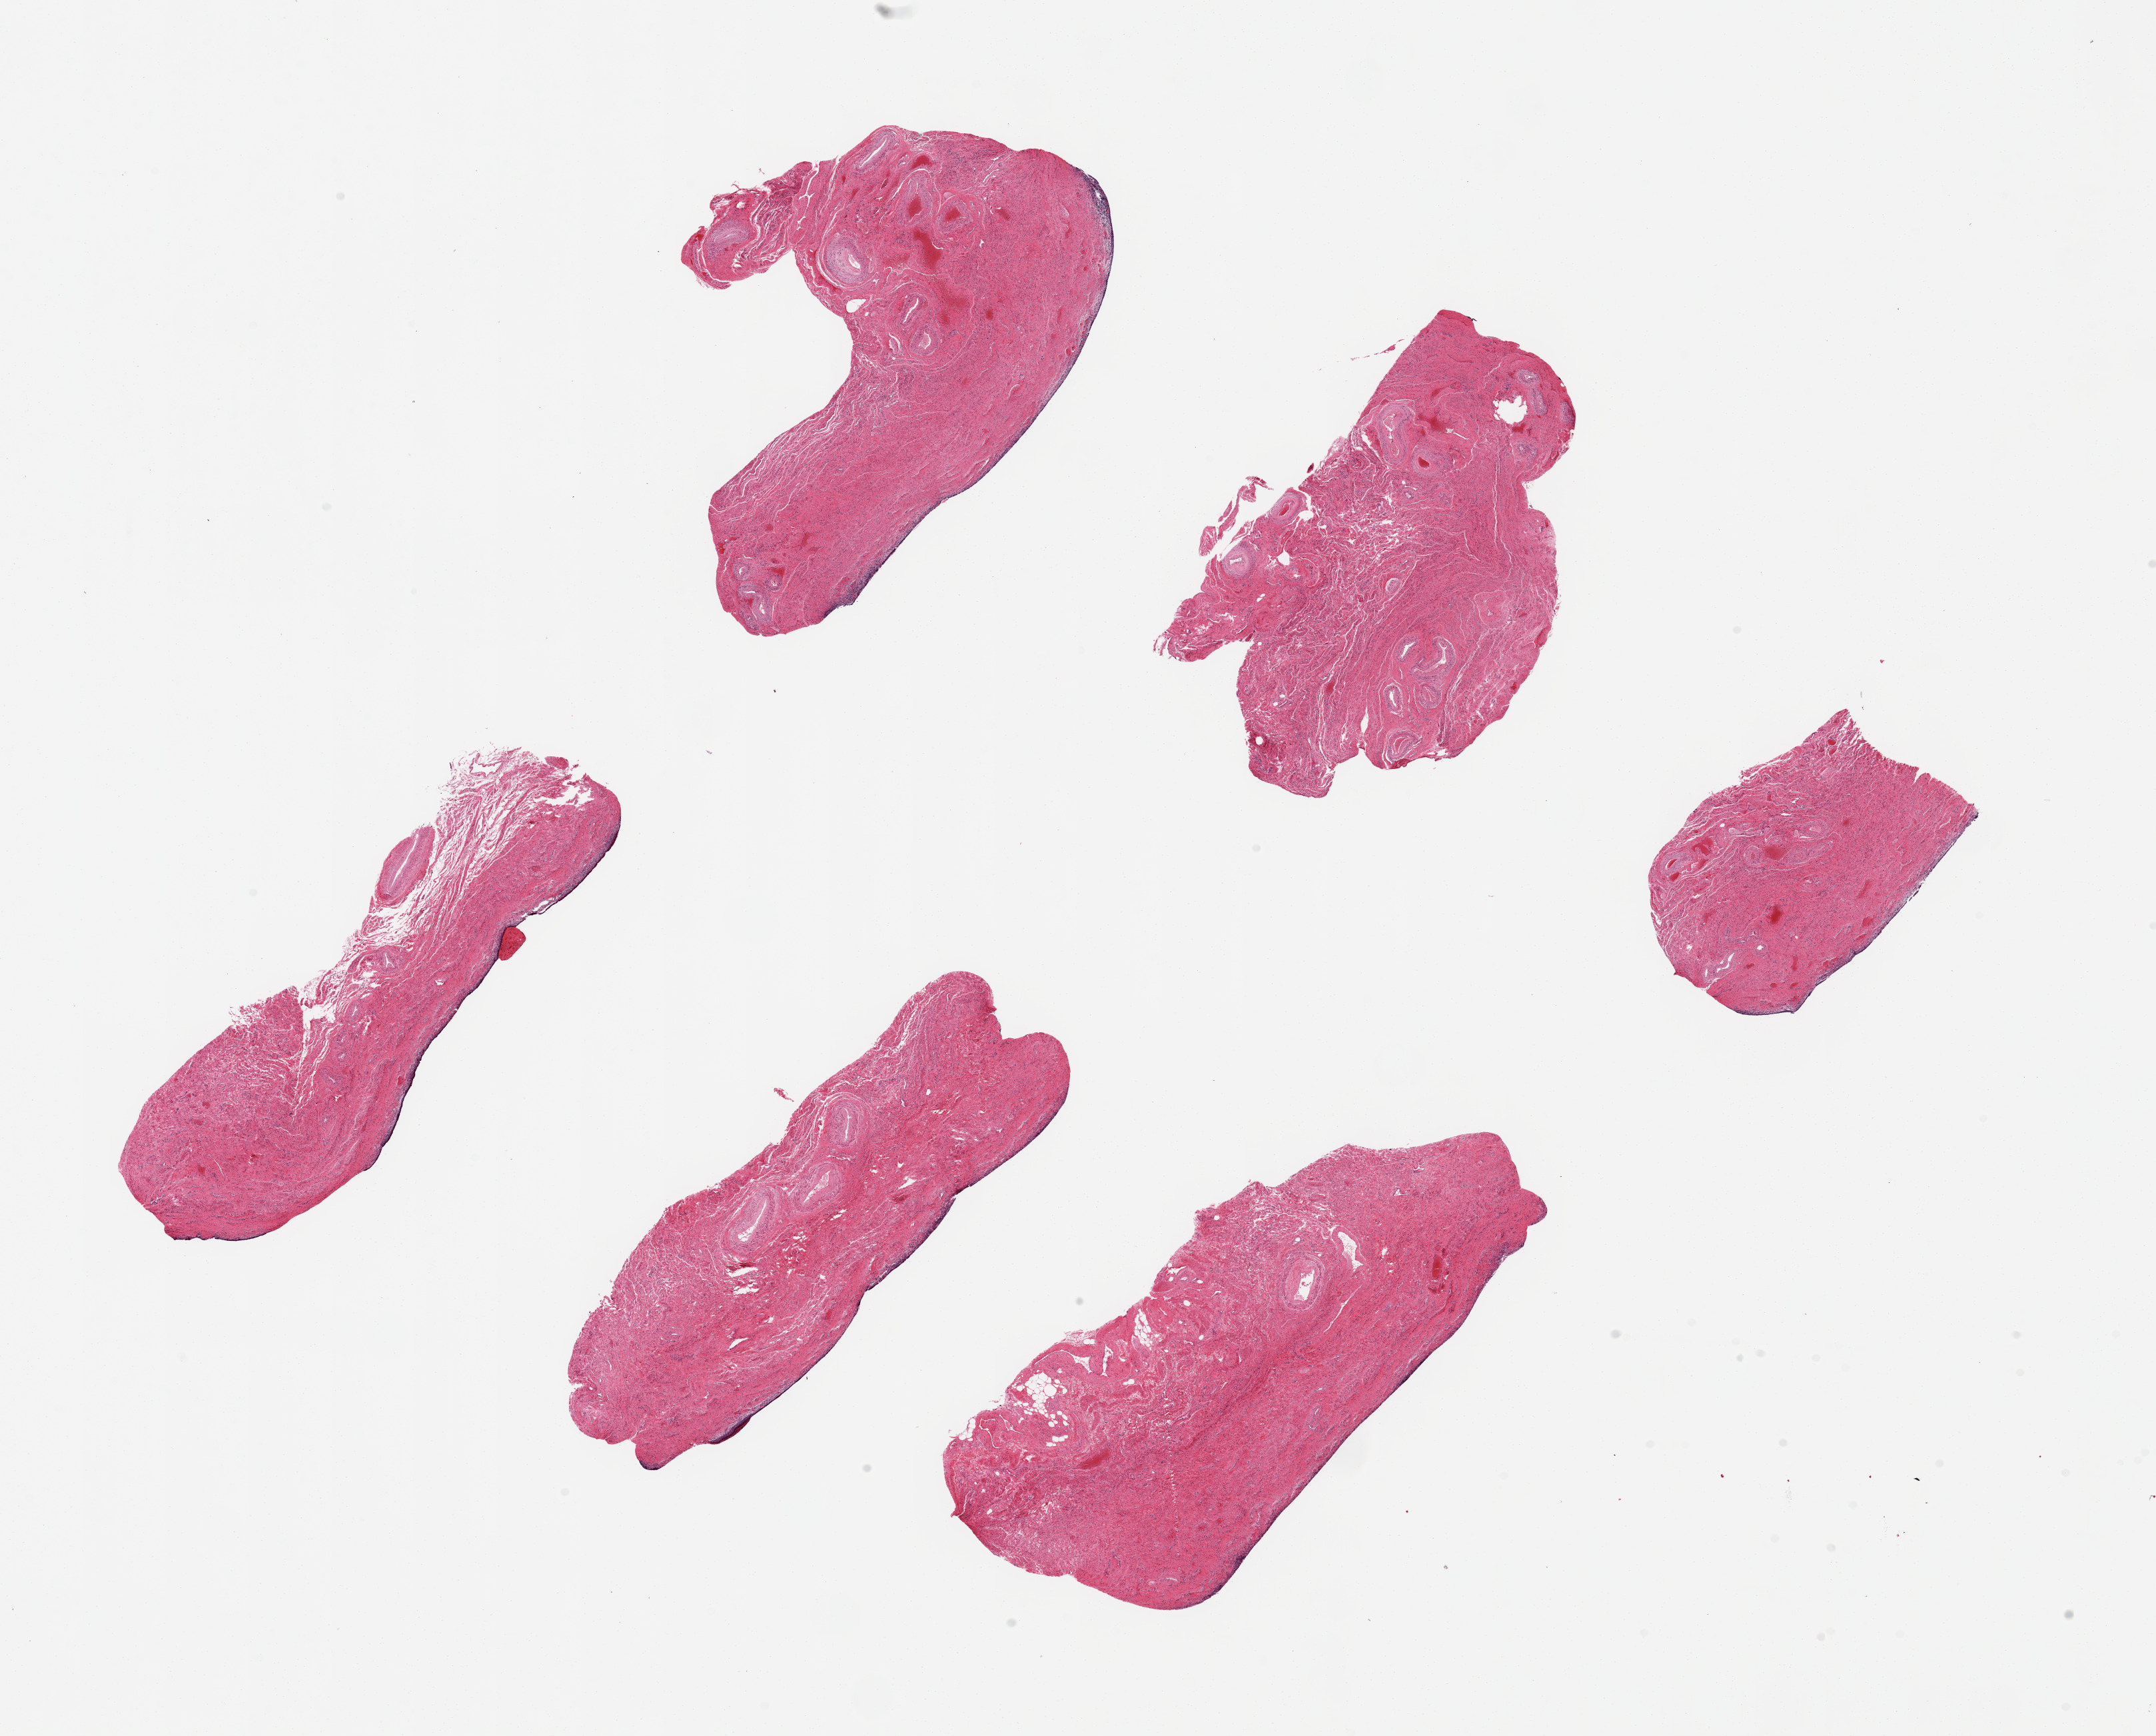
Whole-slide image, haematoxylin and eosin stain, a low-resolution overview of the entire scanned area, about 25.6 x 20.6 mm. PAXgene-fixed, paraffin-embedded tissue. Sampled site (target tissue): vagina. Donor tissue sample.
* review note (as recorded): 6 pieces up to 7x3 mm; atrophic, largely sloughed epithelium